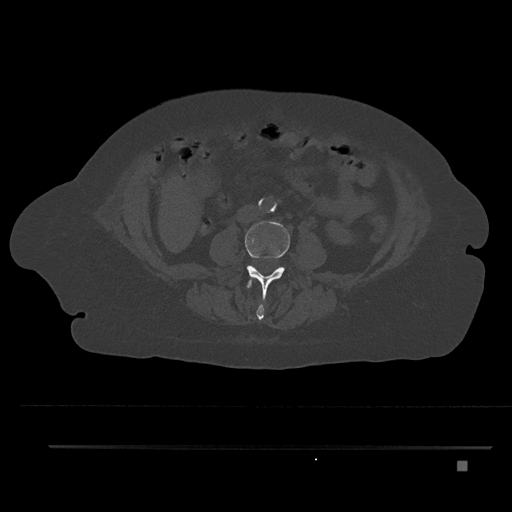
CT including the spine, one axial slice; position 125 of 797 along the scan axis; reconstruction kernel Br40s/3; bone window (W 1800 / L 400 HU); 512 × 512 image matrix. Female patient, age 76 years. Case-level facts recorded for this patient, not image findings: primary cancer: lung.
Structures marked on this image (semi-automatically segmented with operator editing):
- L2 vertebra: bounding box (x1, y1, x2, y2) in pixels: (246, 278, 264, 320)
- L3 vertebra: (239, 221, 310, 304)